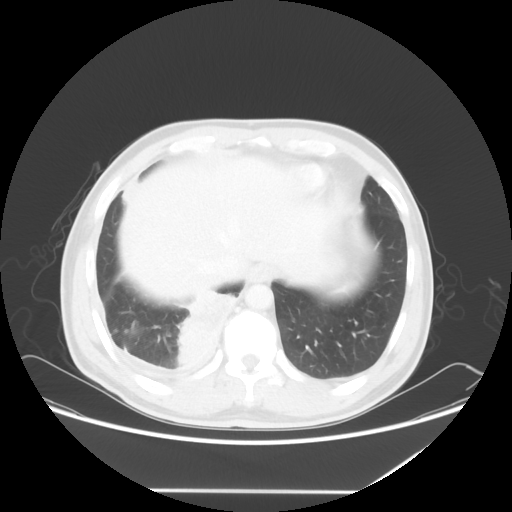
Chest CT, one axial slice. Slice 15 of 60 in the series (ordered by position). Reconstruction kernel STANDARD. 120 kVp. Lung window (W 1500 / L -600 HU). 5 mm slice thickness. 512 × 512 image matrix, field of view 419 × 419 mm. Patient: male, 48 years. From the clinical record (not read from this slice): clinical TNM (as recorded): T3 N3 M1a.
Structures marked on this image (bounding box drawn by a radiologist):
- lung tumour (recorded histology: squamous cell carcinoma): bounding box (x1, y1, x2, y2) in pixels: (176, 284, 240, 368)